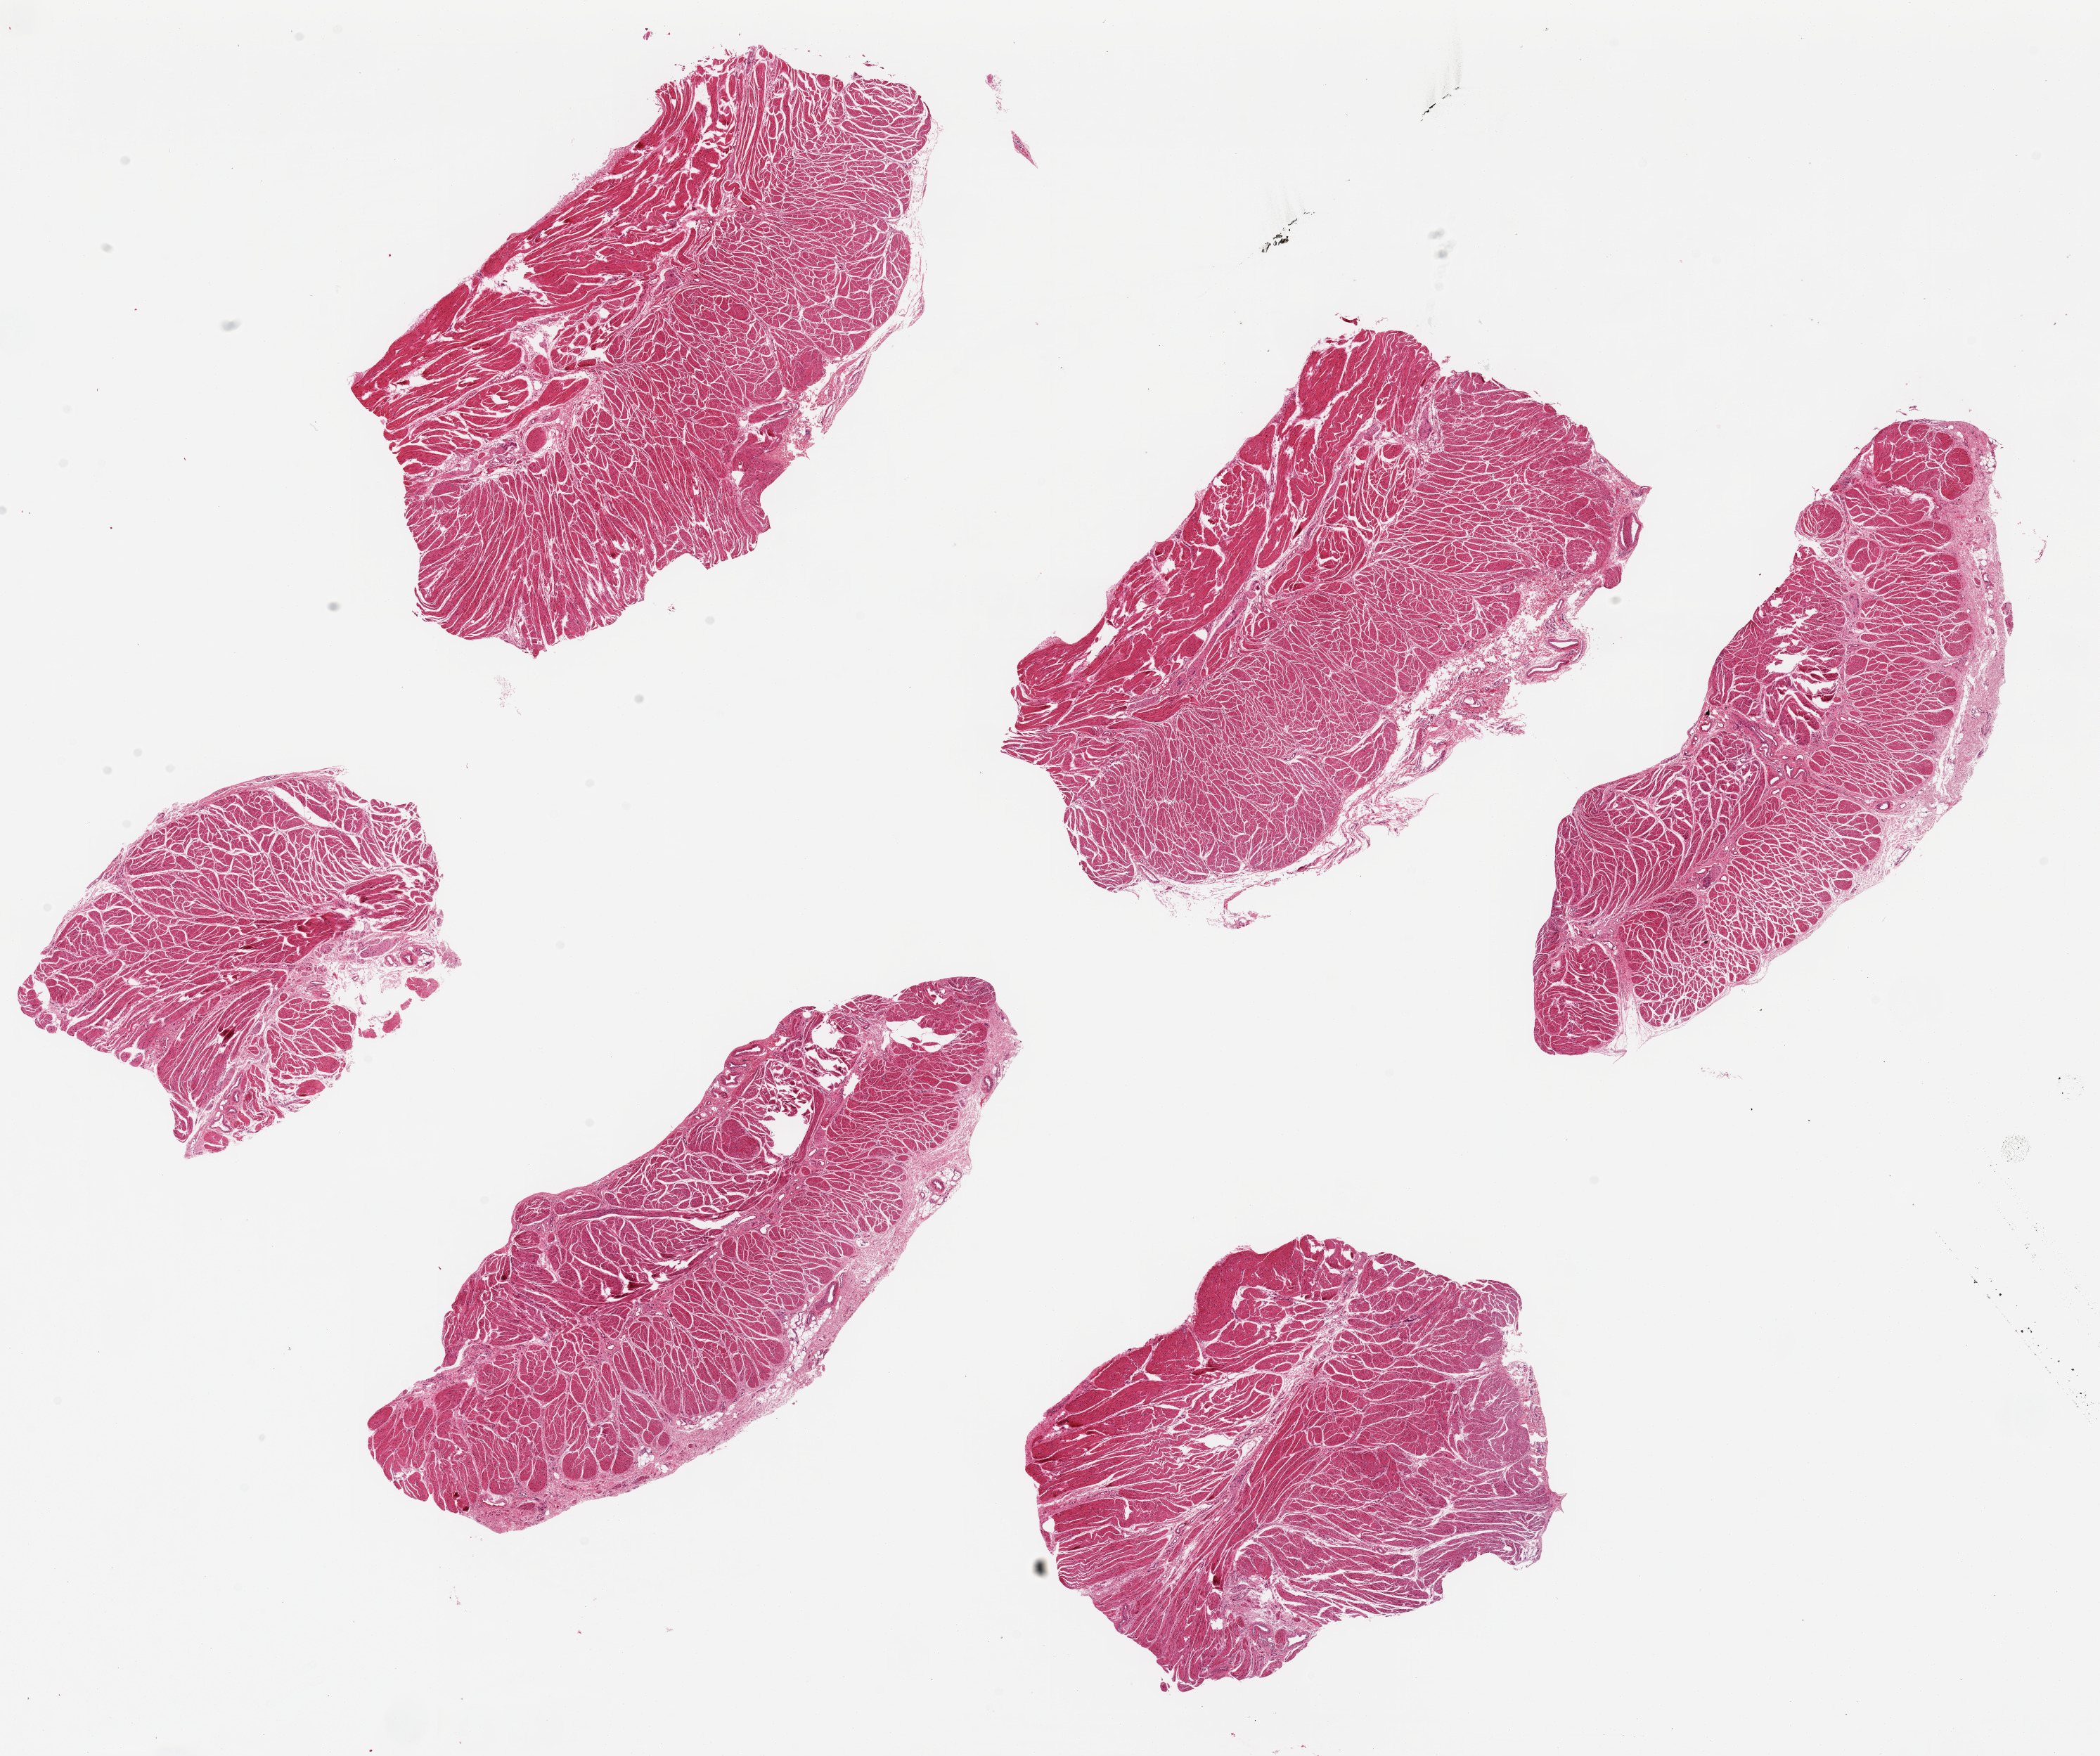
Whole-slide image, haematoxylin and eosin stain — shown as a low-resolution overview of the whole scanned area (about 23.6 x 19.8 mm, from a 20x scan), PAXgene-fixed, paraffin-embedded tissue, section of esophageal muscle (target tissue), tissue donor sample.
Pathologist's review note for this sample: 6 pieces up to 8.7x4.3 mm.